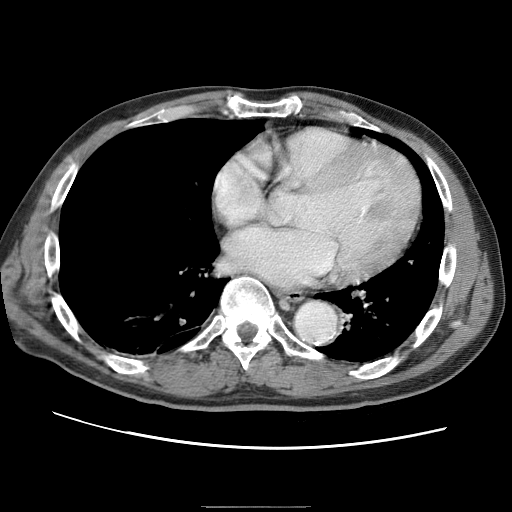
Contrast-enhanced abdominal CT (liver protocol), one axial slice. Slice 73 of 75 in the series (ordered by position). 120 kVp. One of 2 acquisitions stored at this slice position. Soft-tissue window (W 400 / L 40 HU). 512 × 512 image matrix, field of view 360 × 360 mm. Case-level facts recorded for this patient, not image findings: diagnosis: hepatocellular carcinoma (patient treated with transarterial chemoembolisation; whether this scan precedes or follows treatment is not stated here); TNM stage (as recorded): Stage-II; Child-Pugh class: A; tumour differentiation: well differentiated; tumour nodularity: multinodular.
Structures marked on this image (semi-automatically segmented with operator editing):
- liver parenchyma outside the tumour (the mass and vessels are separate outlines, so this box may not span the whole liver): box from (x=104, y=198) to (x=148, y=256) px
- liver vessels: (x=121, y=238)–(x=125, y=242)